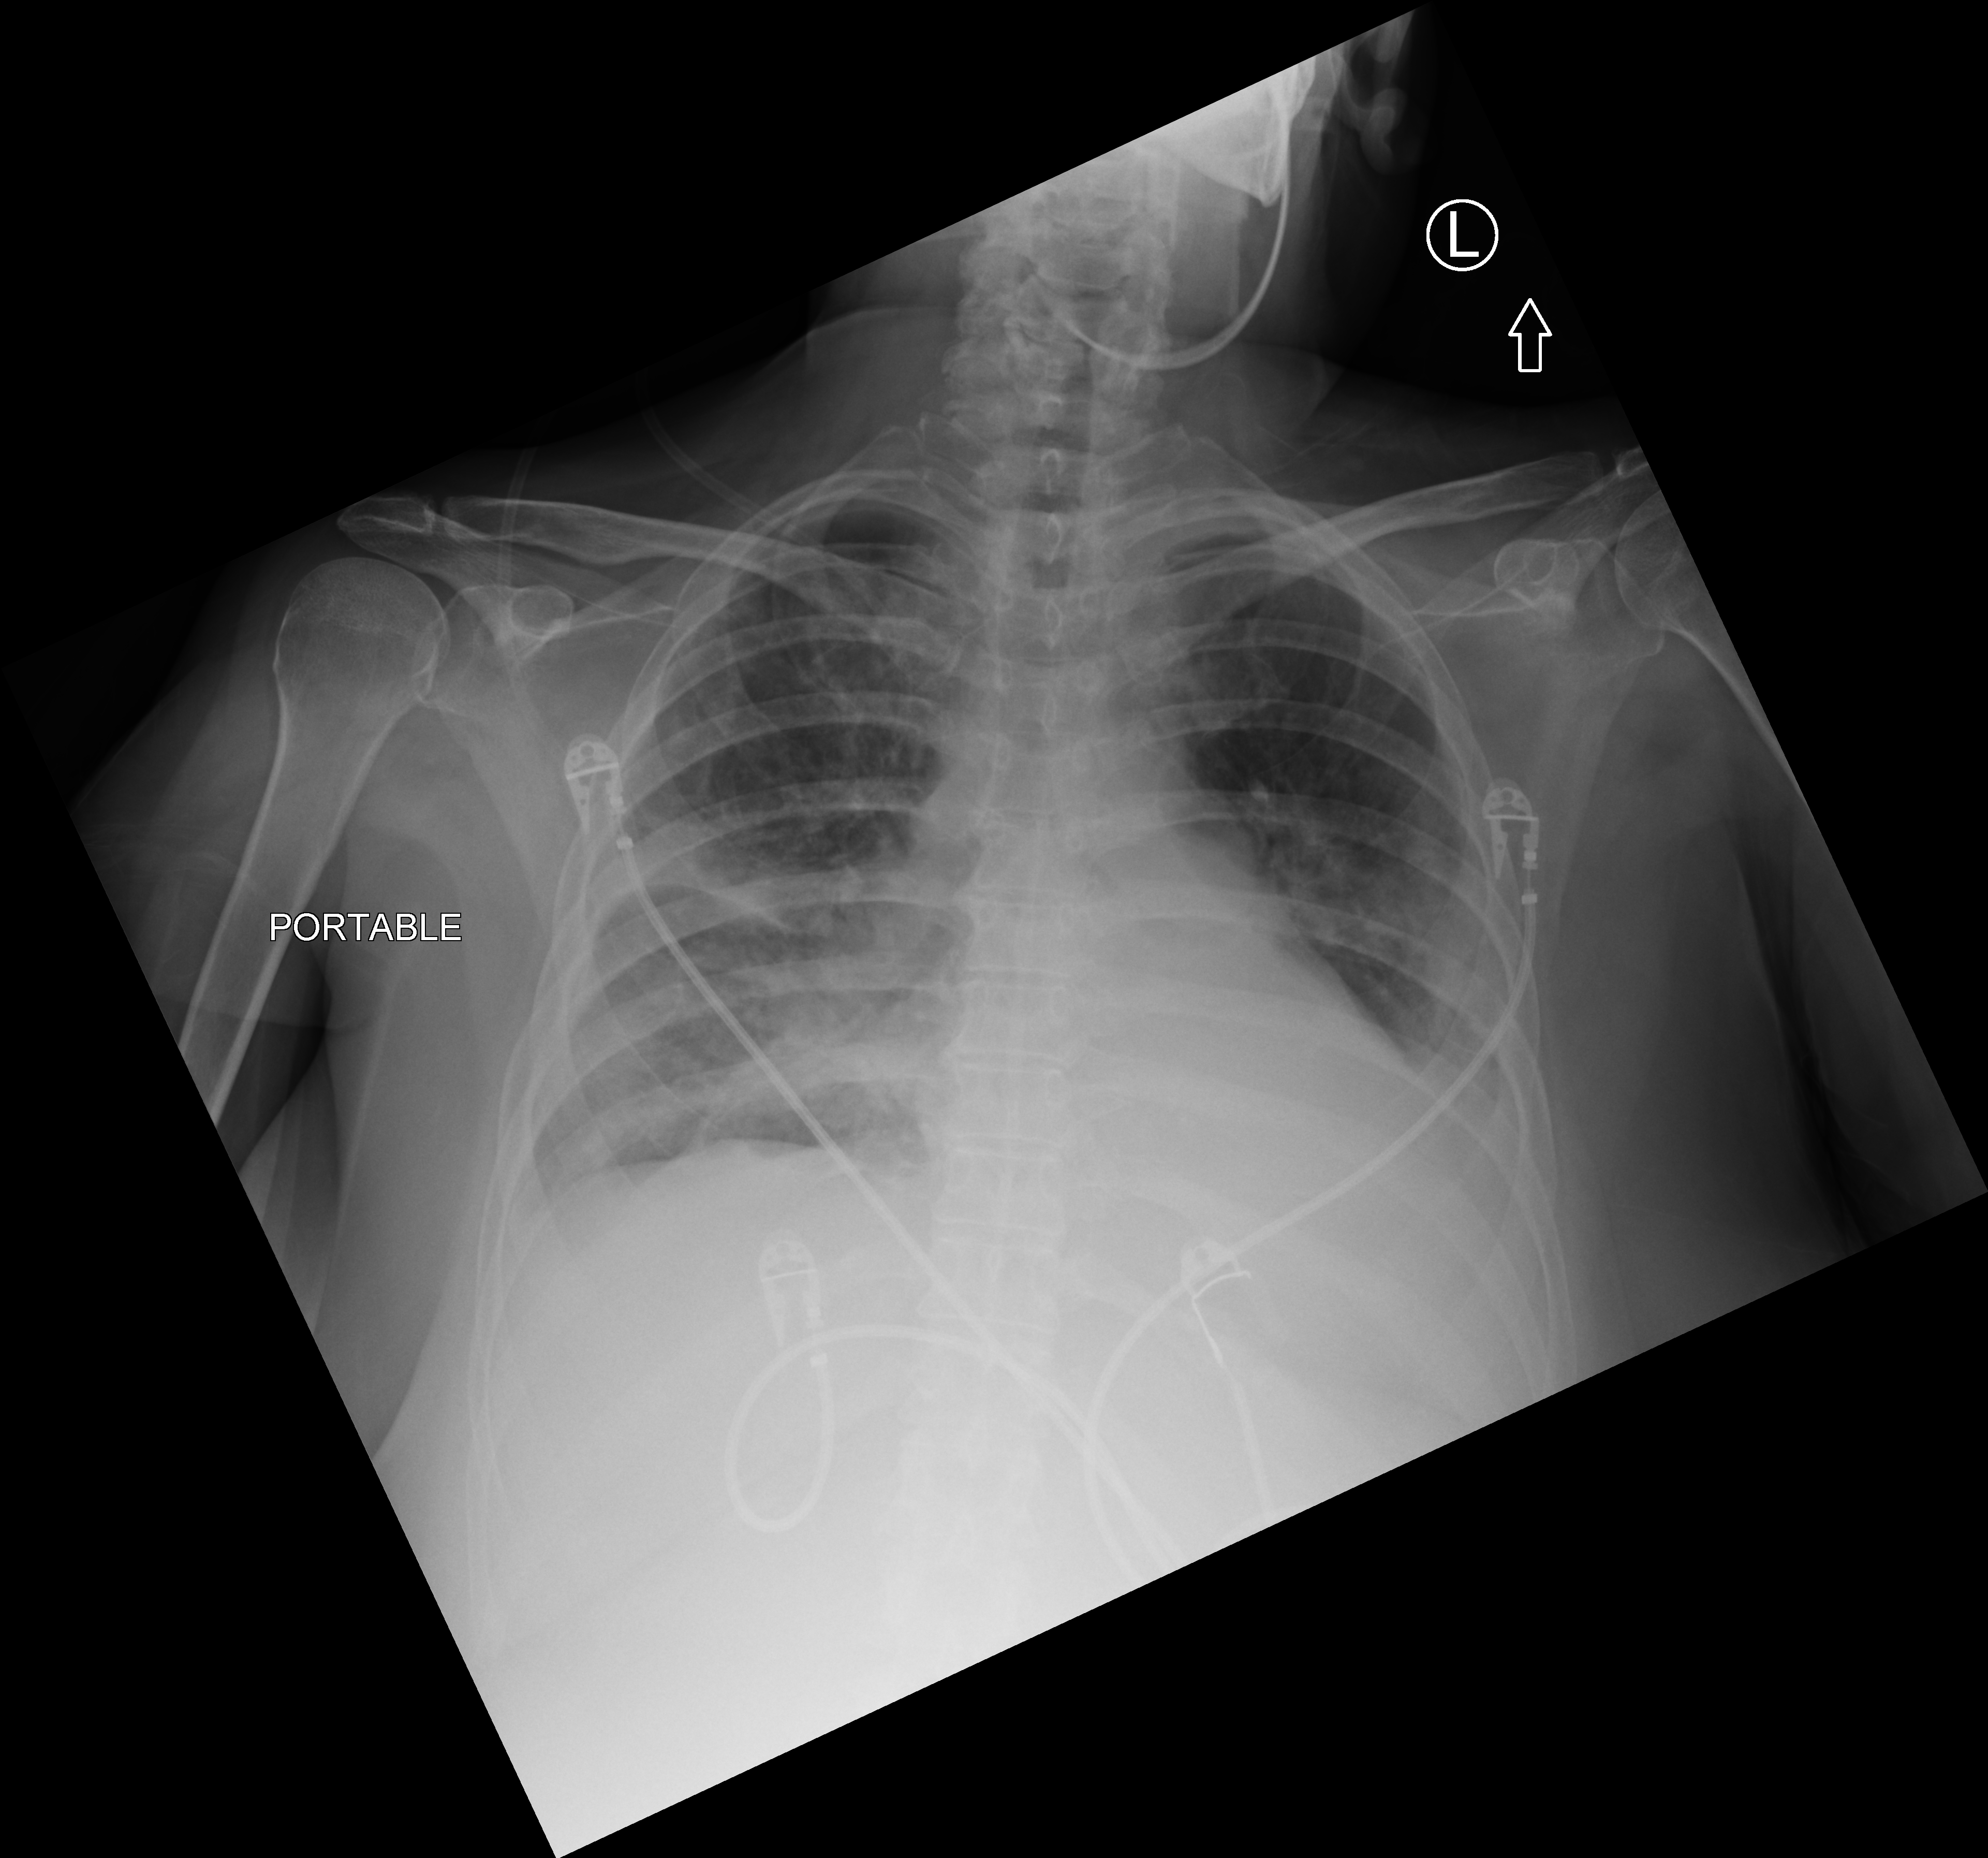
Portable chest radiograph, anteroposterior (AP) projection. Female patient hospitalised with COVID-19, age 60–74 years.
From the hospital-stay record, not from the radiograph (when in the stay this image was taken is not recorded): mechanically ventilated during this hospital stay: yes; admitted to intensive care during this hospital stay: yes.